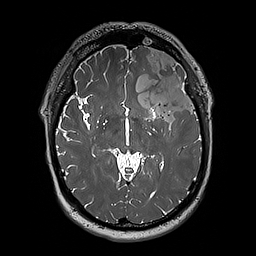
Brain MRI from a brain-tumour surgery series, one axial slice; slice 118 of 192 in the series (ordered by position); 1 mm slice thickness; 256 × 256 image matrix, field of view 250 × 250 mm. Case-level facts recorded for this patient, not image findings: histopathology: Oligodendroglioma; WHO grade: 3; IDH mutation: yes; tumour location: Left Sylvian Fissure (Temporal).
Structures marked on this image (outlined manually by an expert reader):
- tumour: bounding box [x1, y1, x2, y2] px = [124, 49, 197, 122]